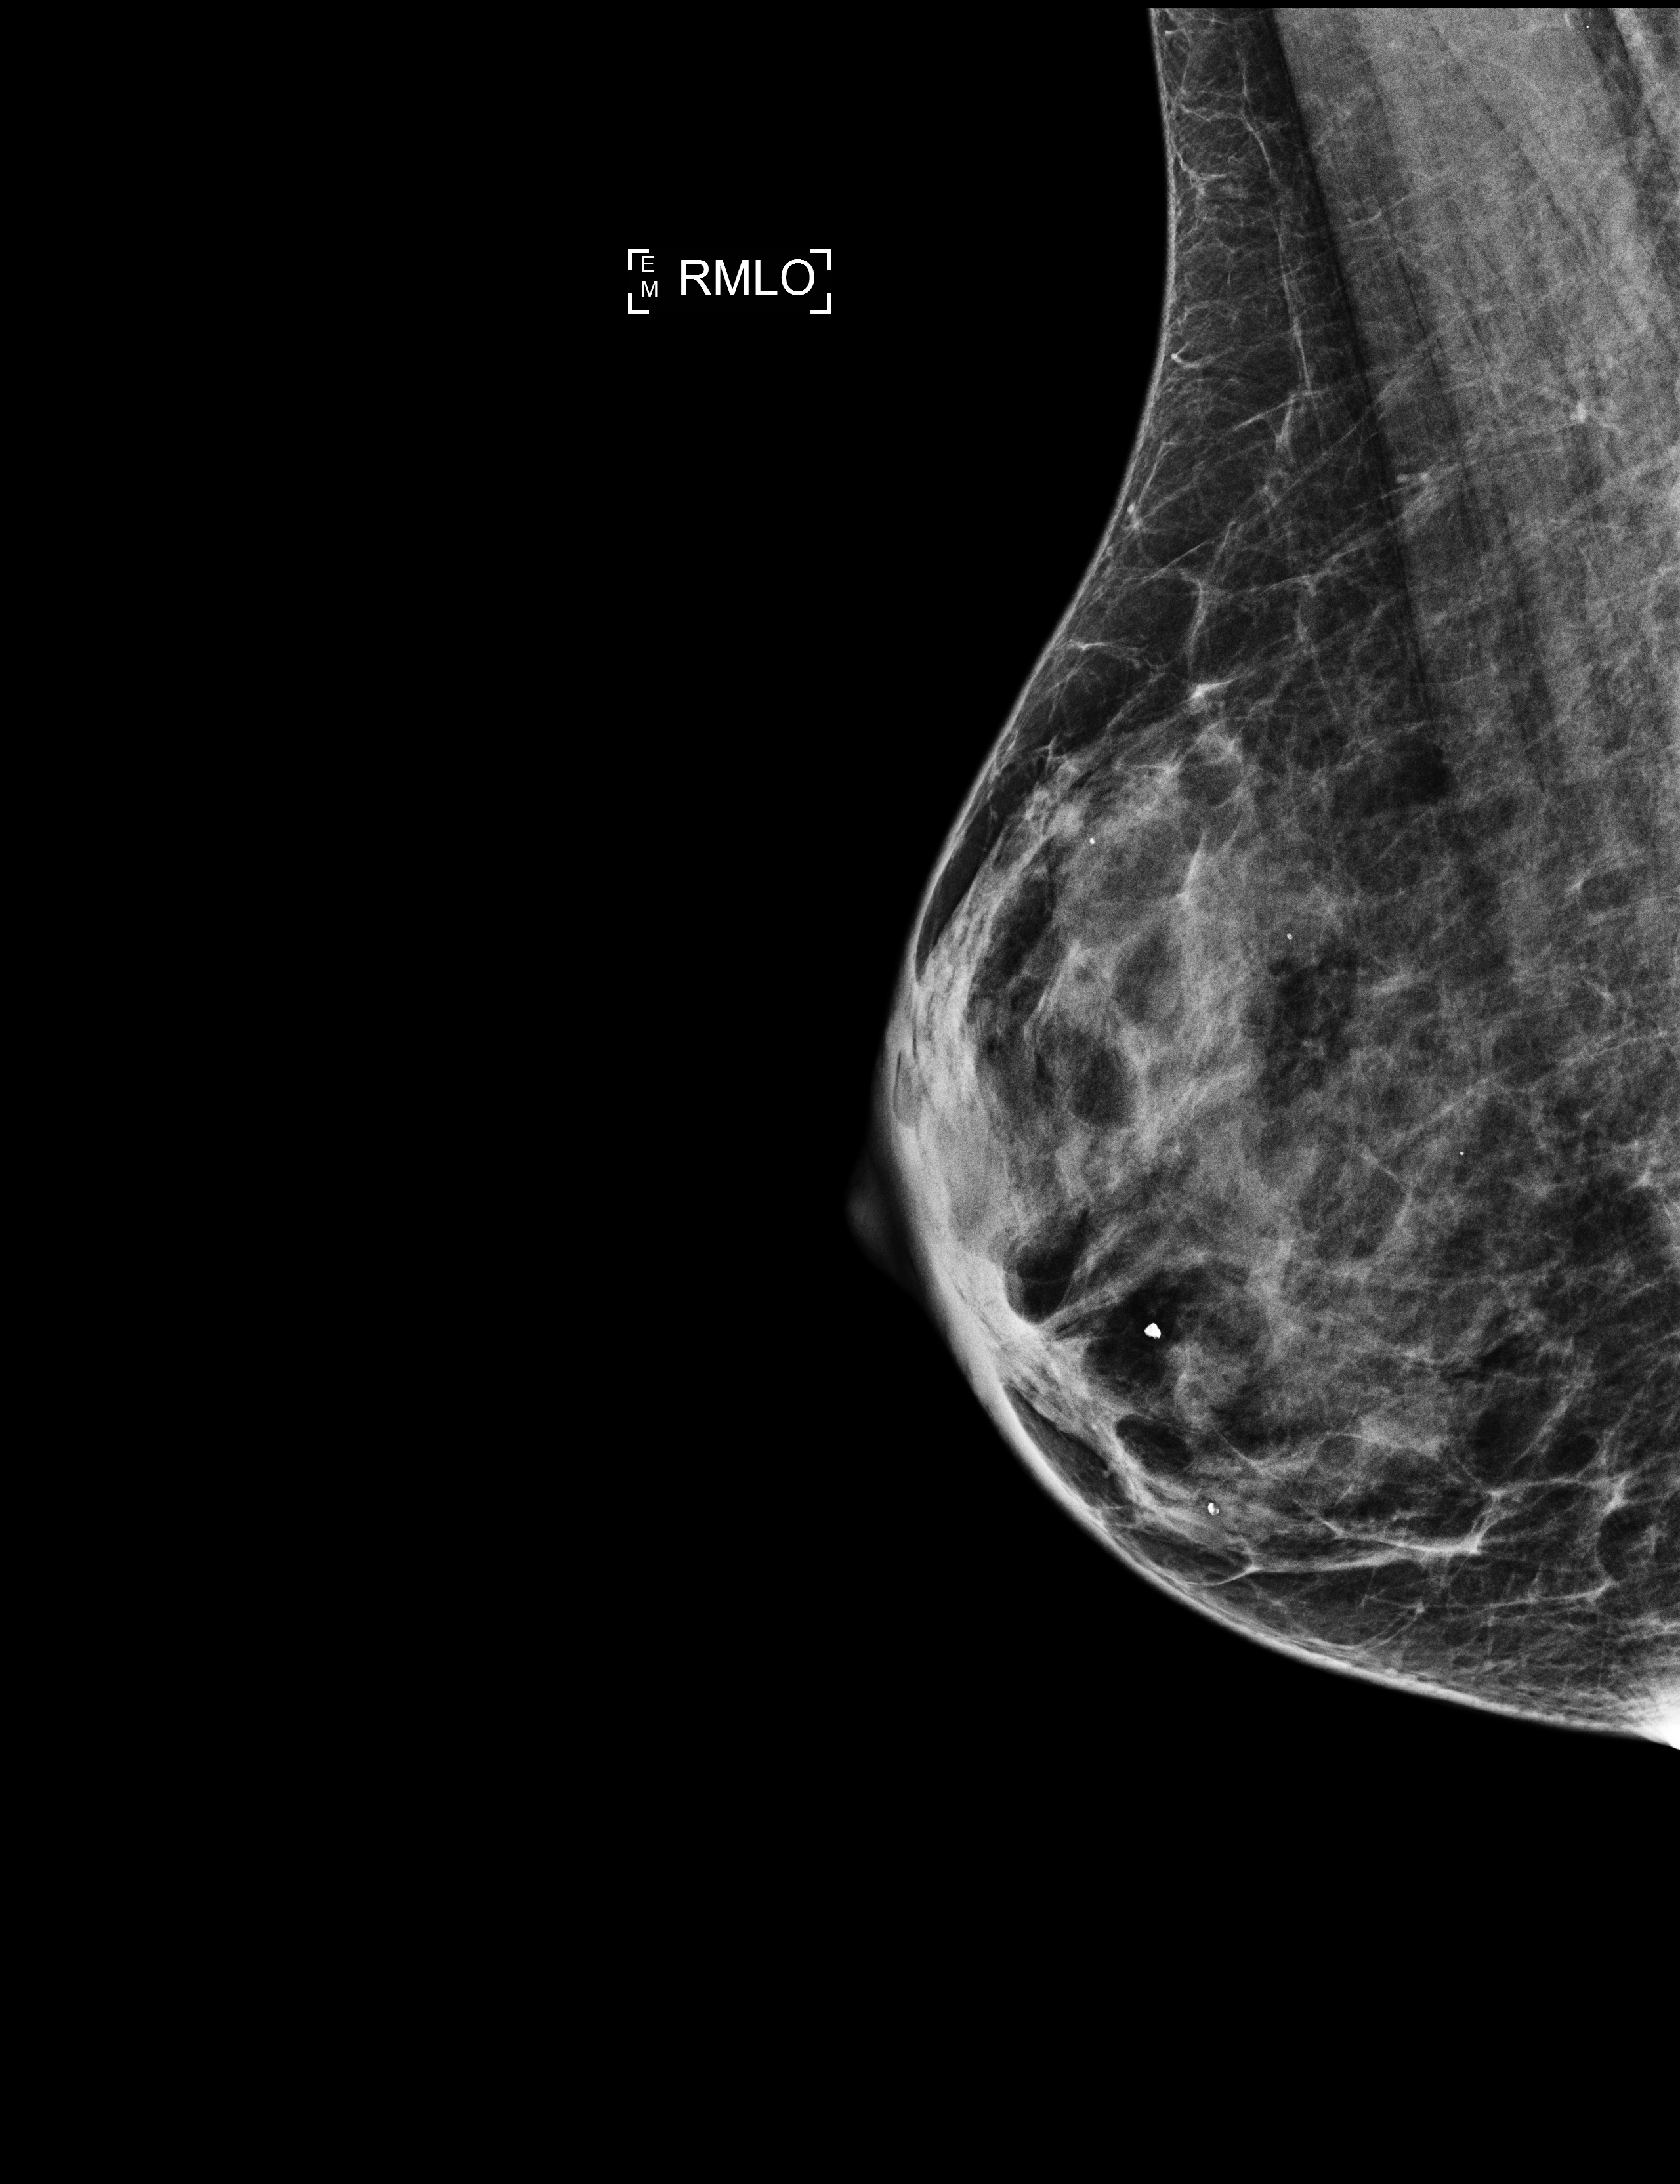
Screening examination, compressed breast thickness 36 mm. Patient: female, 66 years.
Image type: full-field digital mammogram. Breast: right. Projection: MLO view.